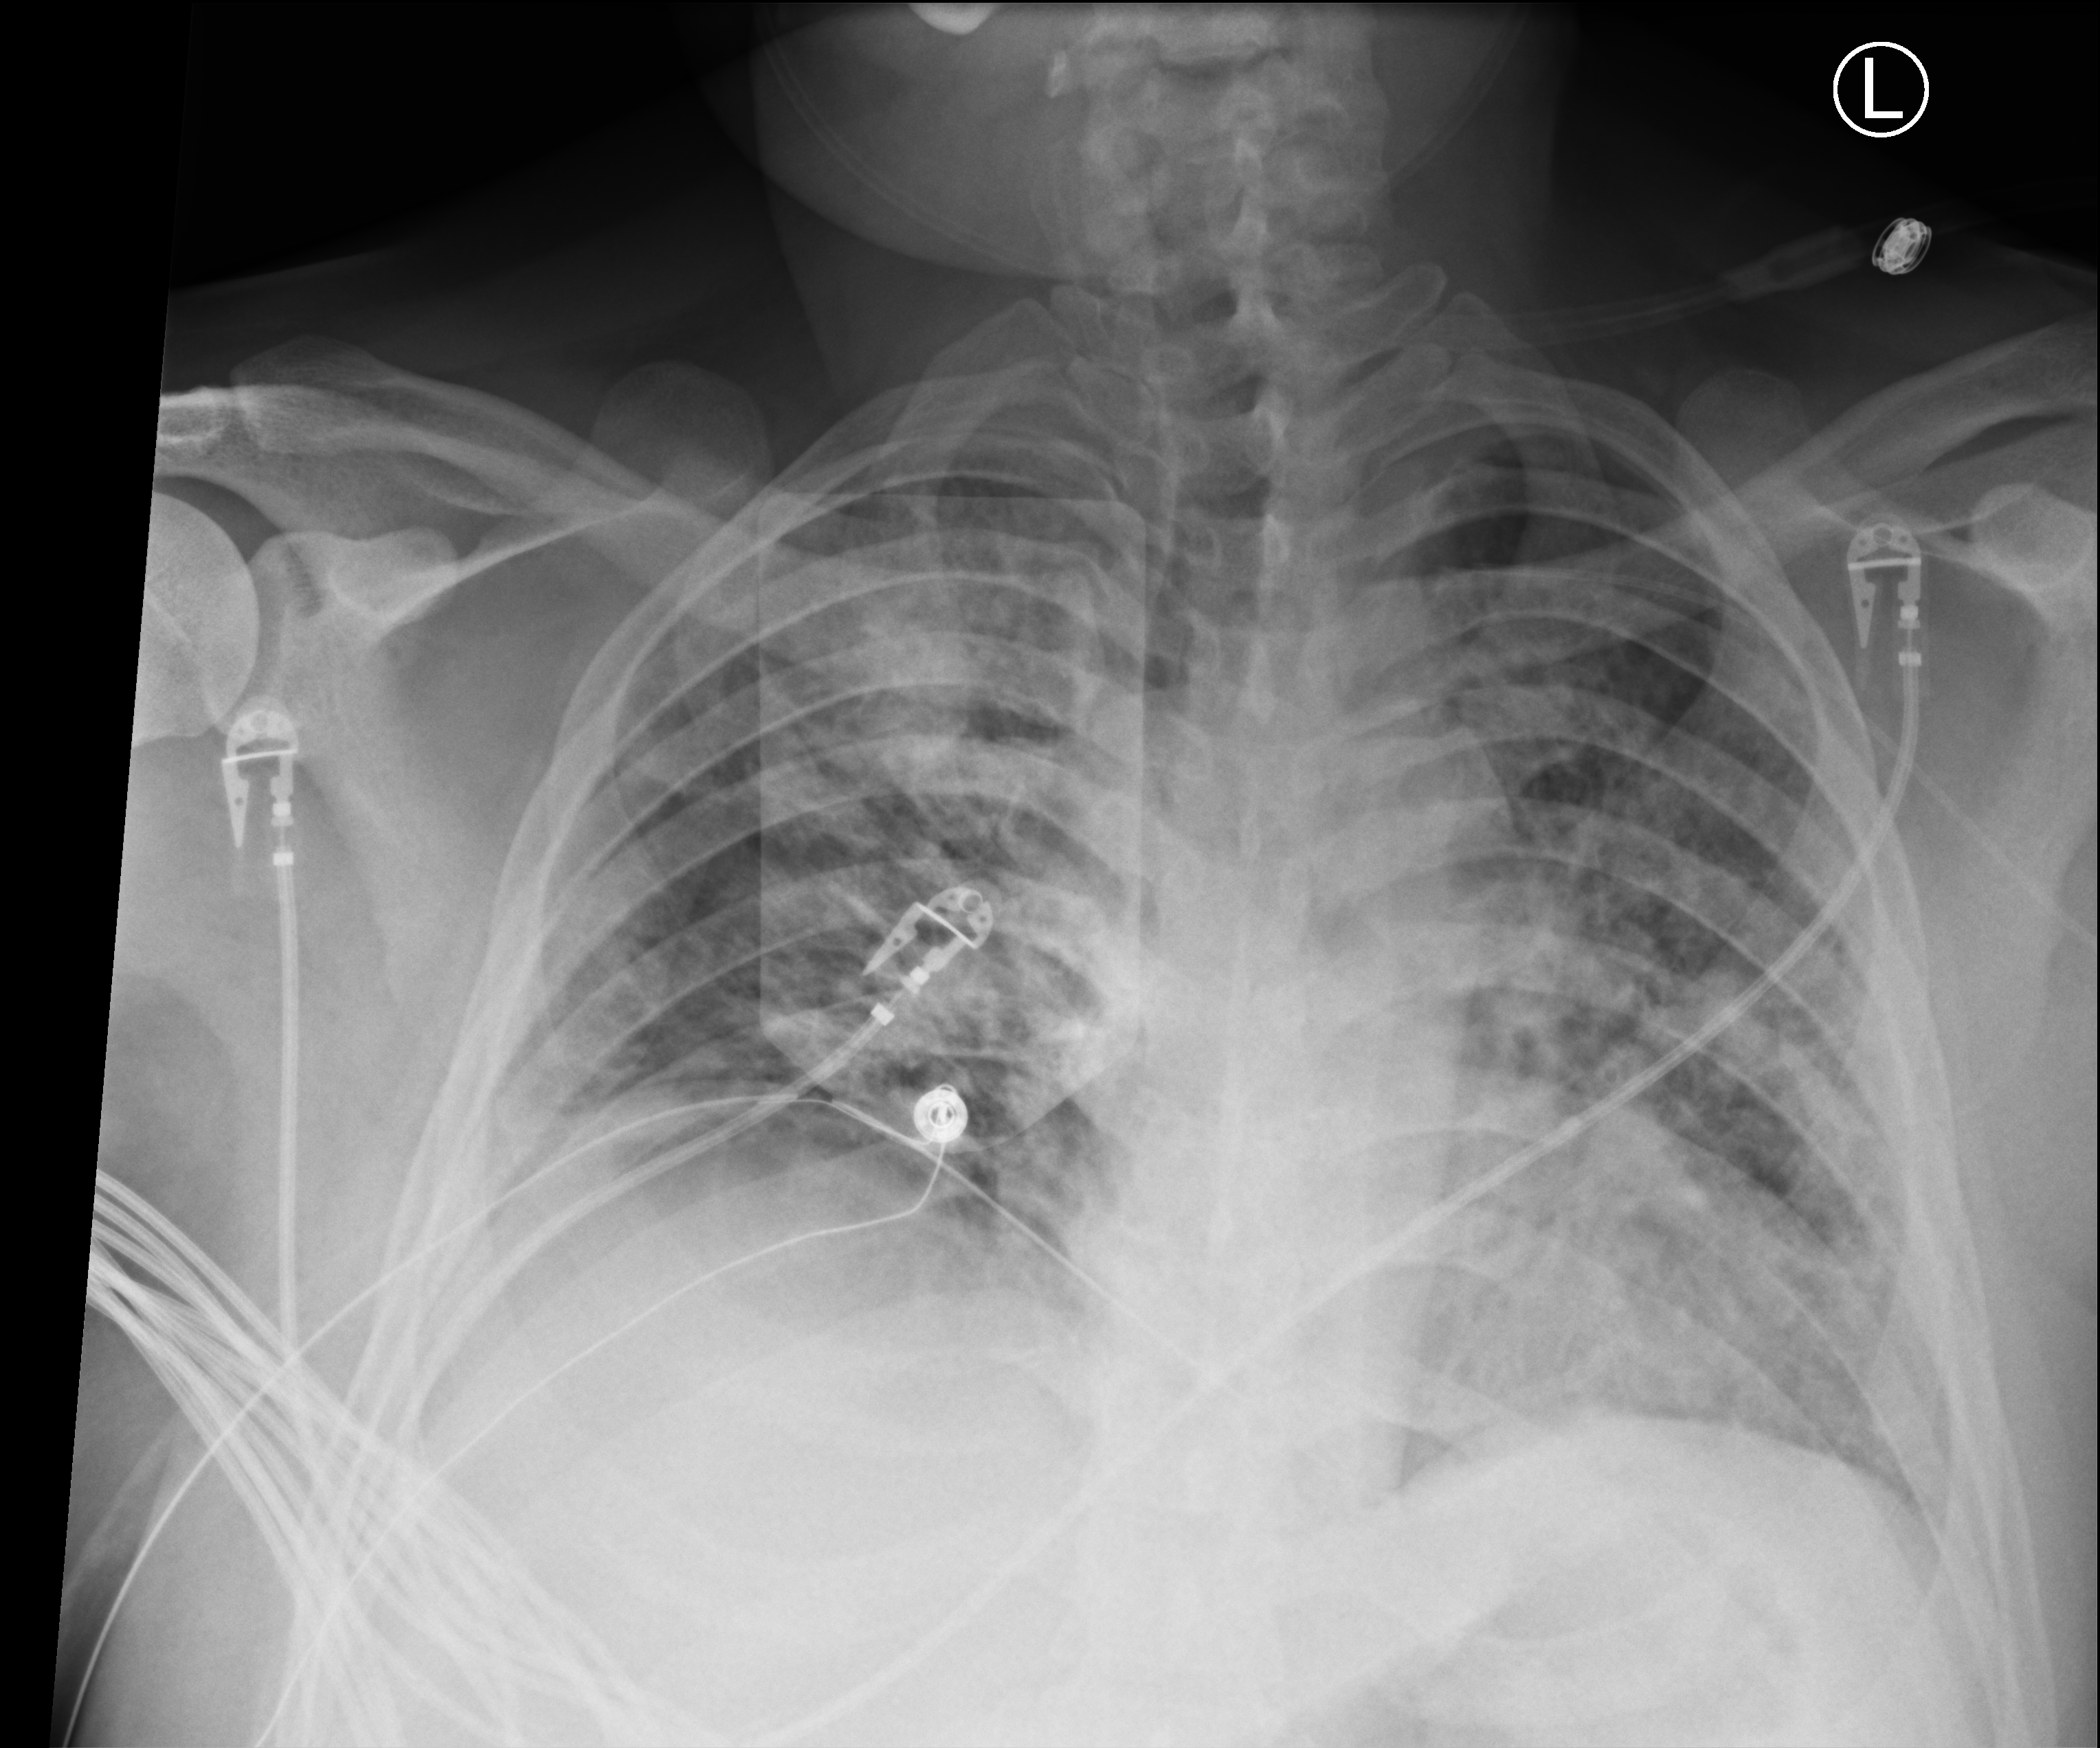
Chest X-ray (portable). Male patient hospitalised with COVID-19, age 18–59 years.
Hospital-stay facts (about this admission, not read from this image; timing relative to this image not recorded): mechanically ventilated during this hospital stay: yes; admitted to intensive care during this hospital stay: yes.